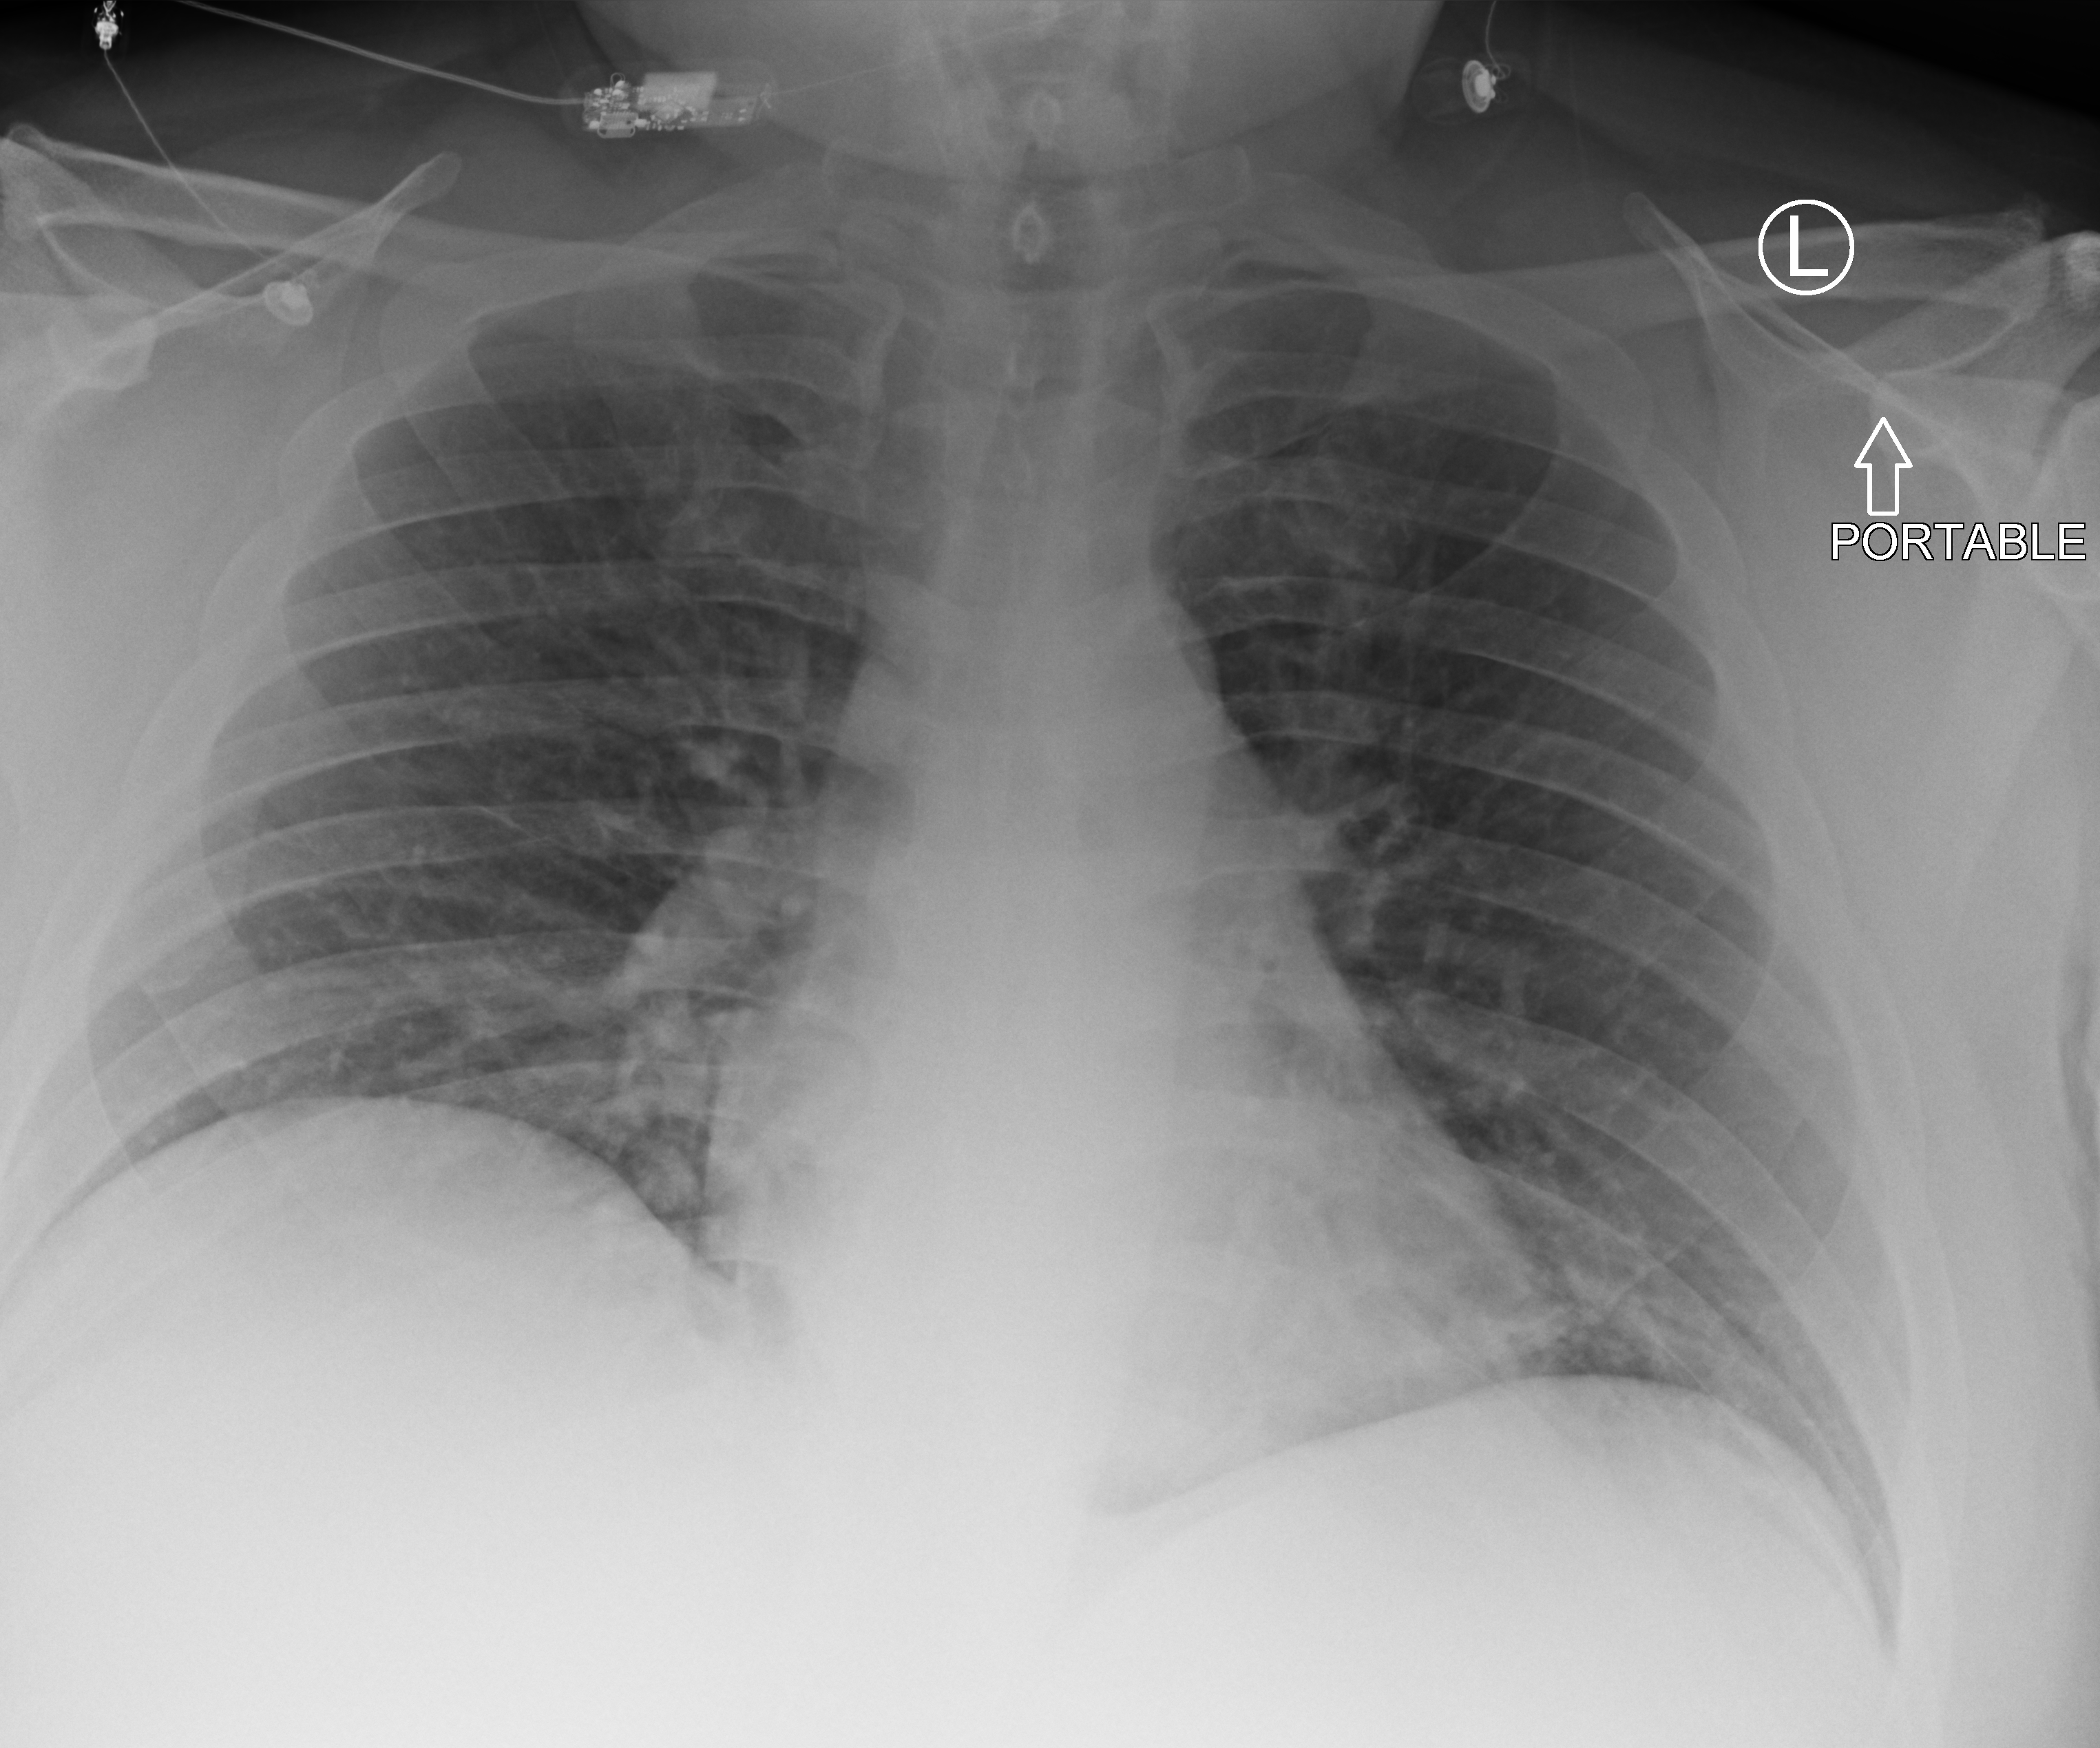
Chest X-ray (portable), anteroposterior (AP) projection. Patient hospitalised with COVID-19; male, aged 18–59 years.
Hospital-stay facts (about this admission, not read from this image; timing relative to this image not recorded):
- length of hospital stay: 6 days
- admitted to intensive care during this hospital stay: no
- mechanically ventilated during this hospital stay: no